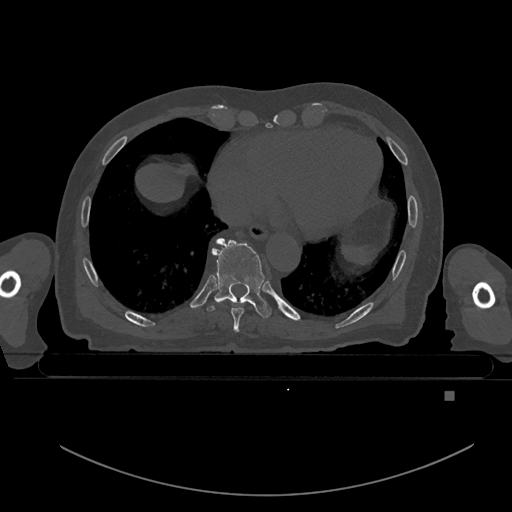
CT including the spine, one axial slice. Slice 164 of 969 in the series (ordered by position). Bone window (W 1800 / L 400 HU). 0.5 mm slice thickness. 512 × 512 image matrix. Male patient, age 82 years. Case-level facts recorded for this patient, not image findings: primary cancer: prostate; vertebrae with lytic lesions (as recorded): T11, T9, T8, T2.
Annotated regions visible in this slice (semi-automatic segmentation, software-assisted and operator-edited):
- T8 vertebra: bounding box (x1, y1, x2, y2) in pixels: (218, 299, 248, 332)
- T9 vertebra: (207, 237, 272, 318)